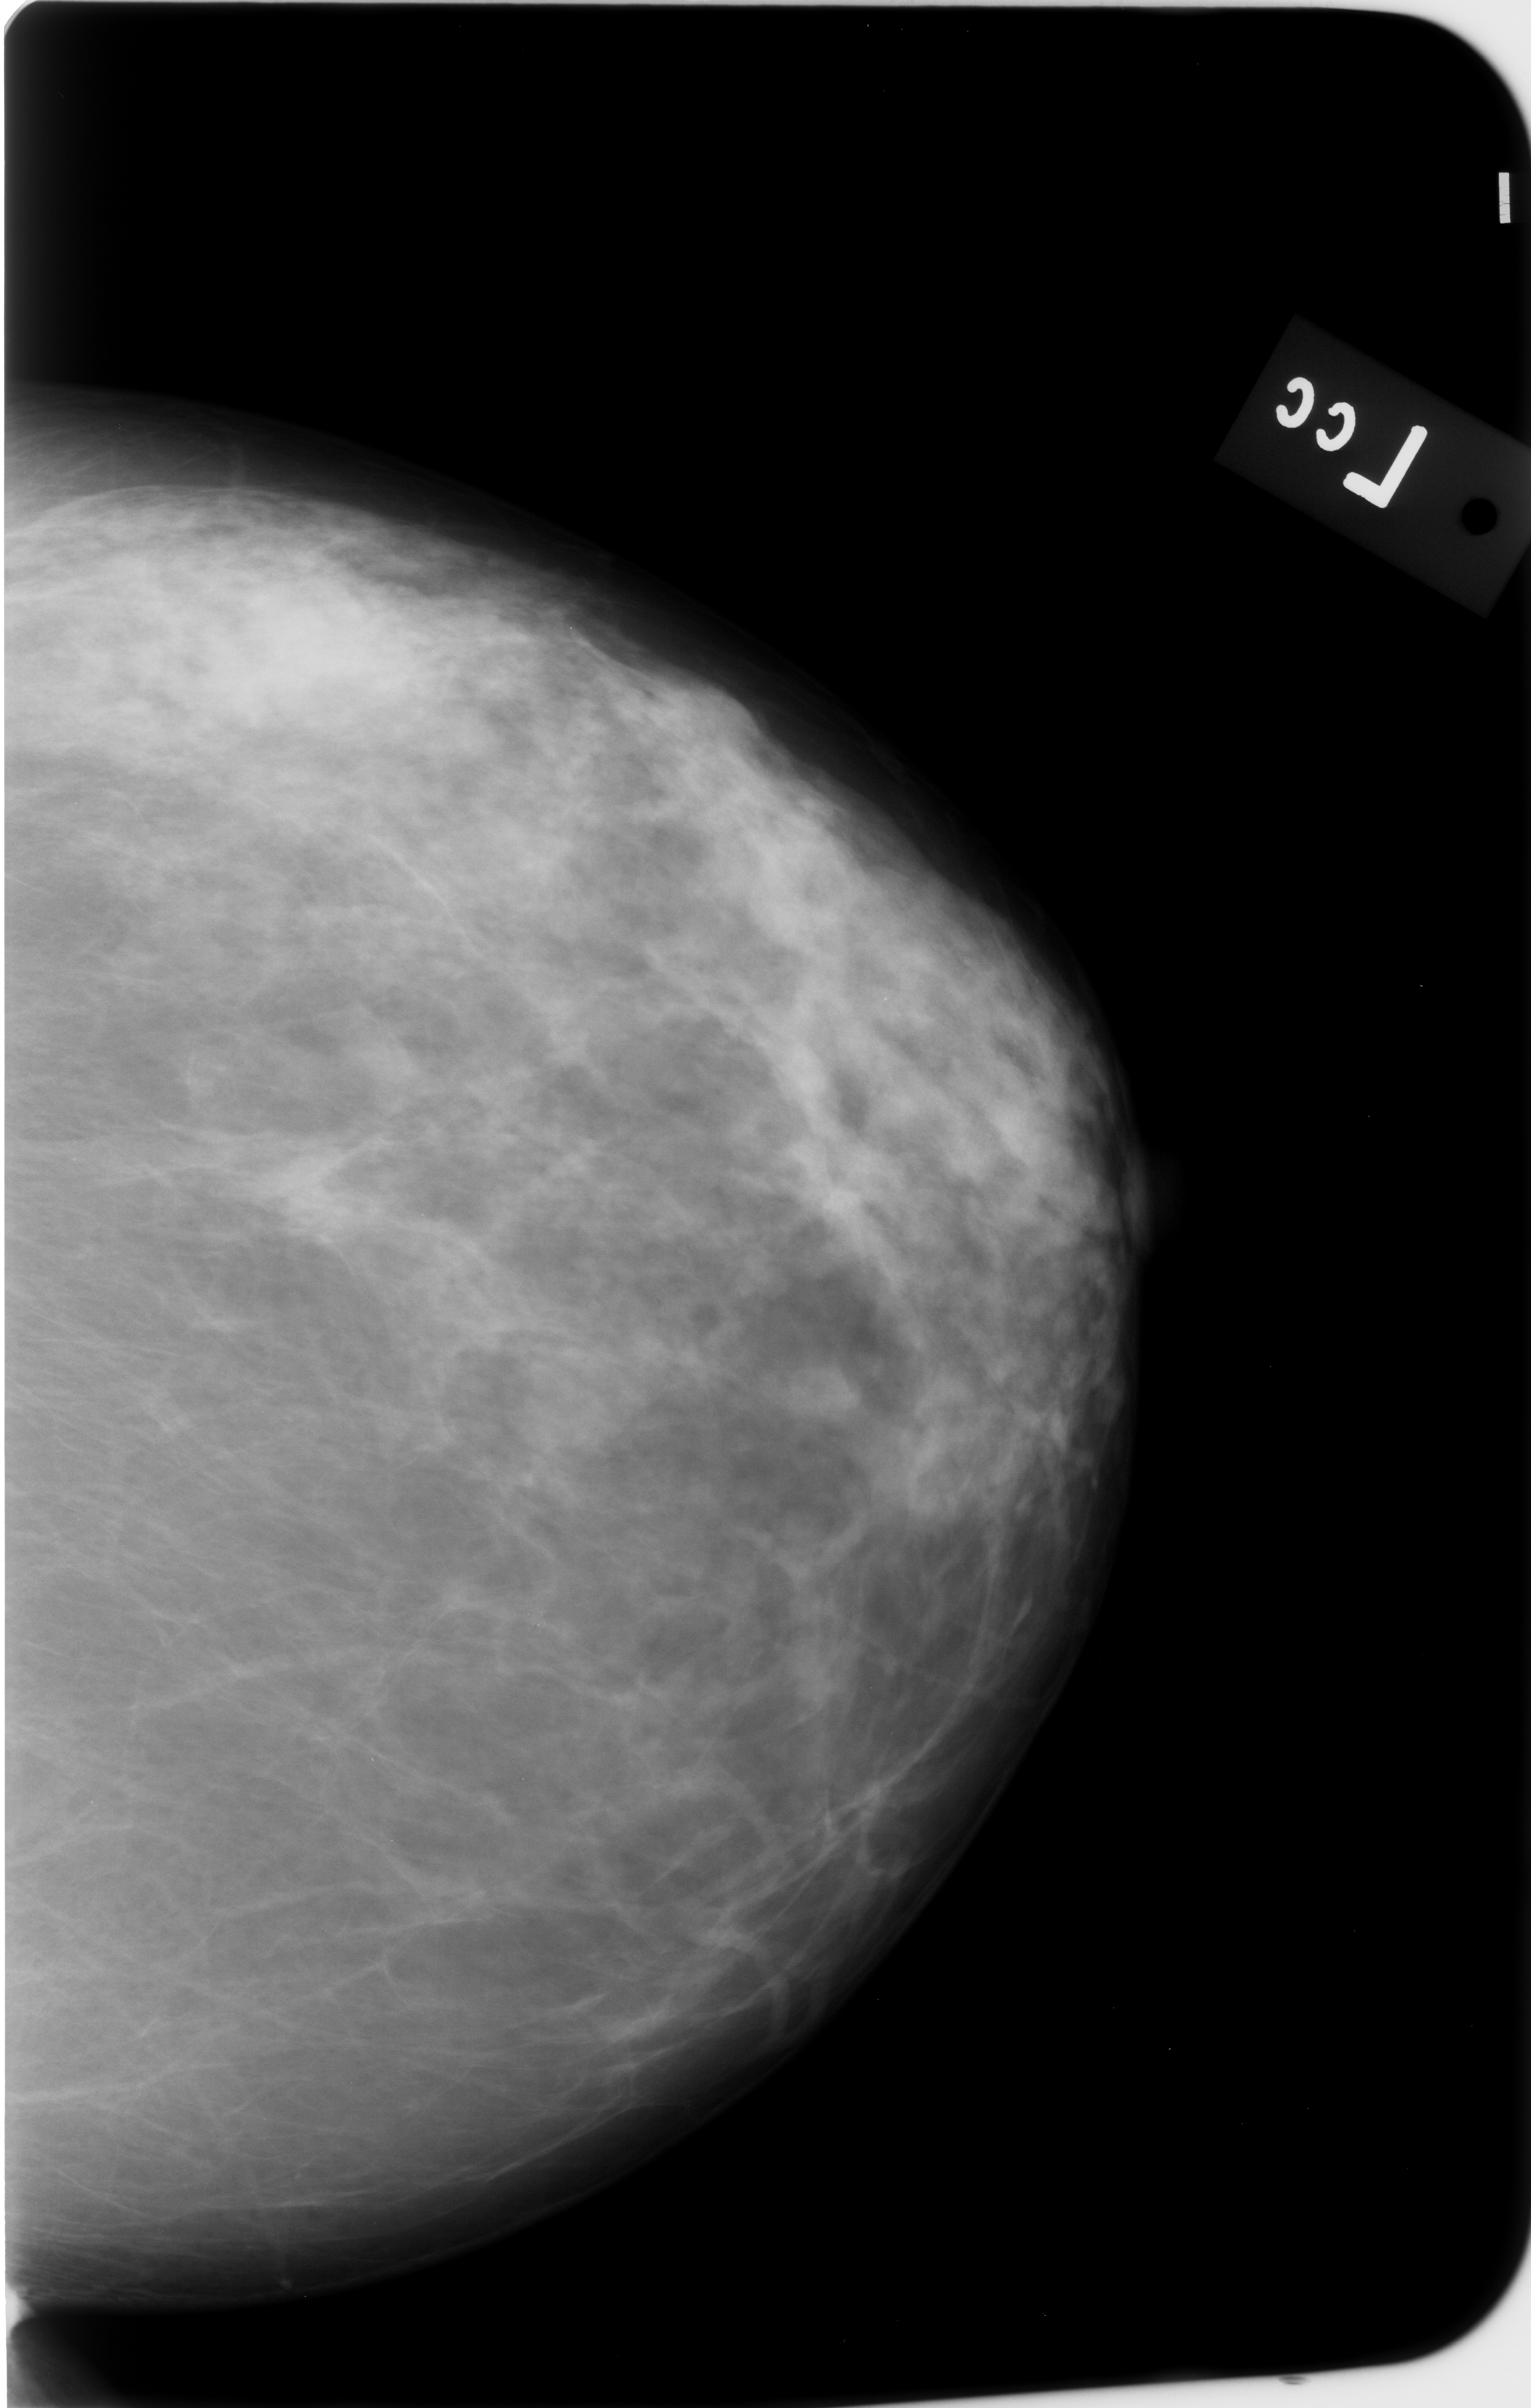
Scanned film-screen mammogram; left breast; craniocaudal (CC) view; breast composition: scattered fibroglandular densities (BI-RADS density category 2 of 4); 1531 × 2408 image matrix.
Expert-marked regions of interest on this image (one box per marked abnormality):
- calcifications, morphology pleomorphic, distribution clustered; BI-RADS assessment category 4; pathology (as recorded): benign: bounding box <493,1590,575,1665> (left, top, right, bottom; pixels)